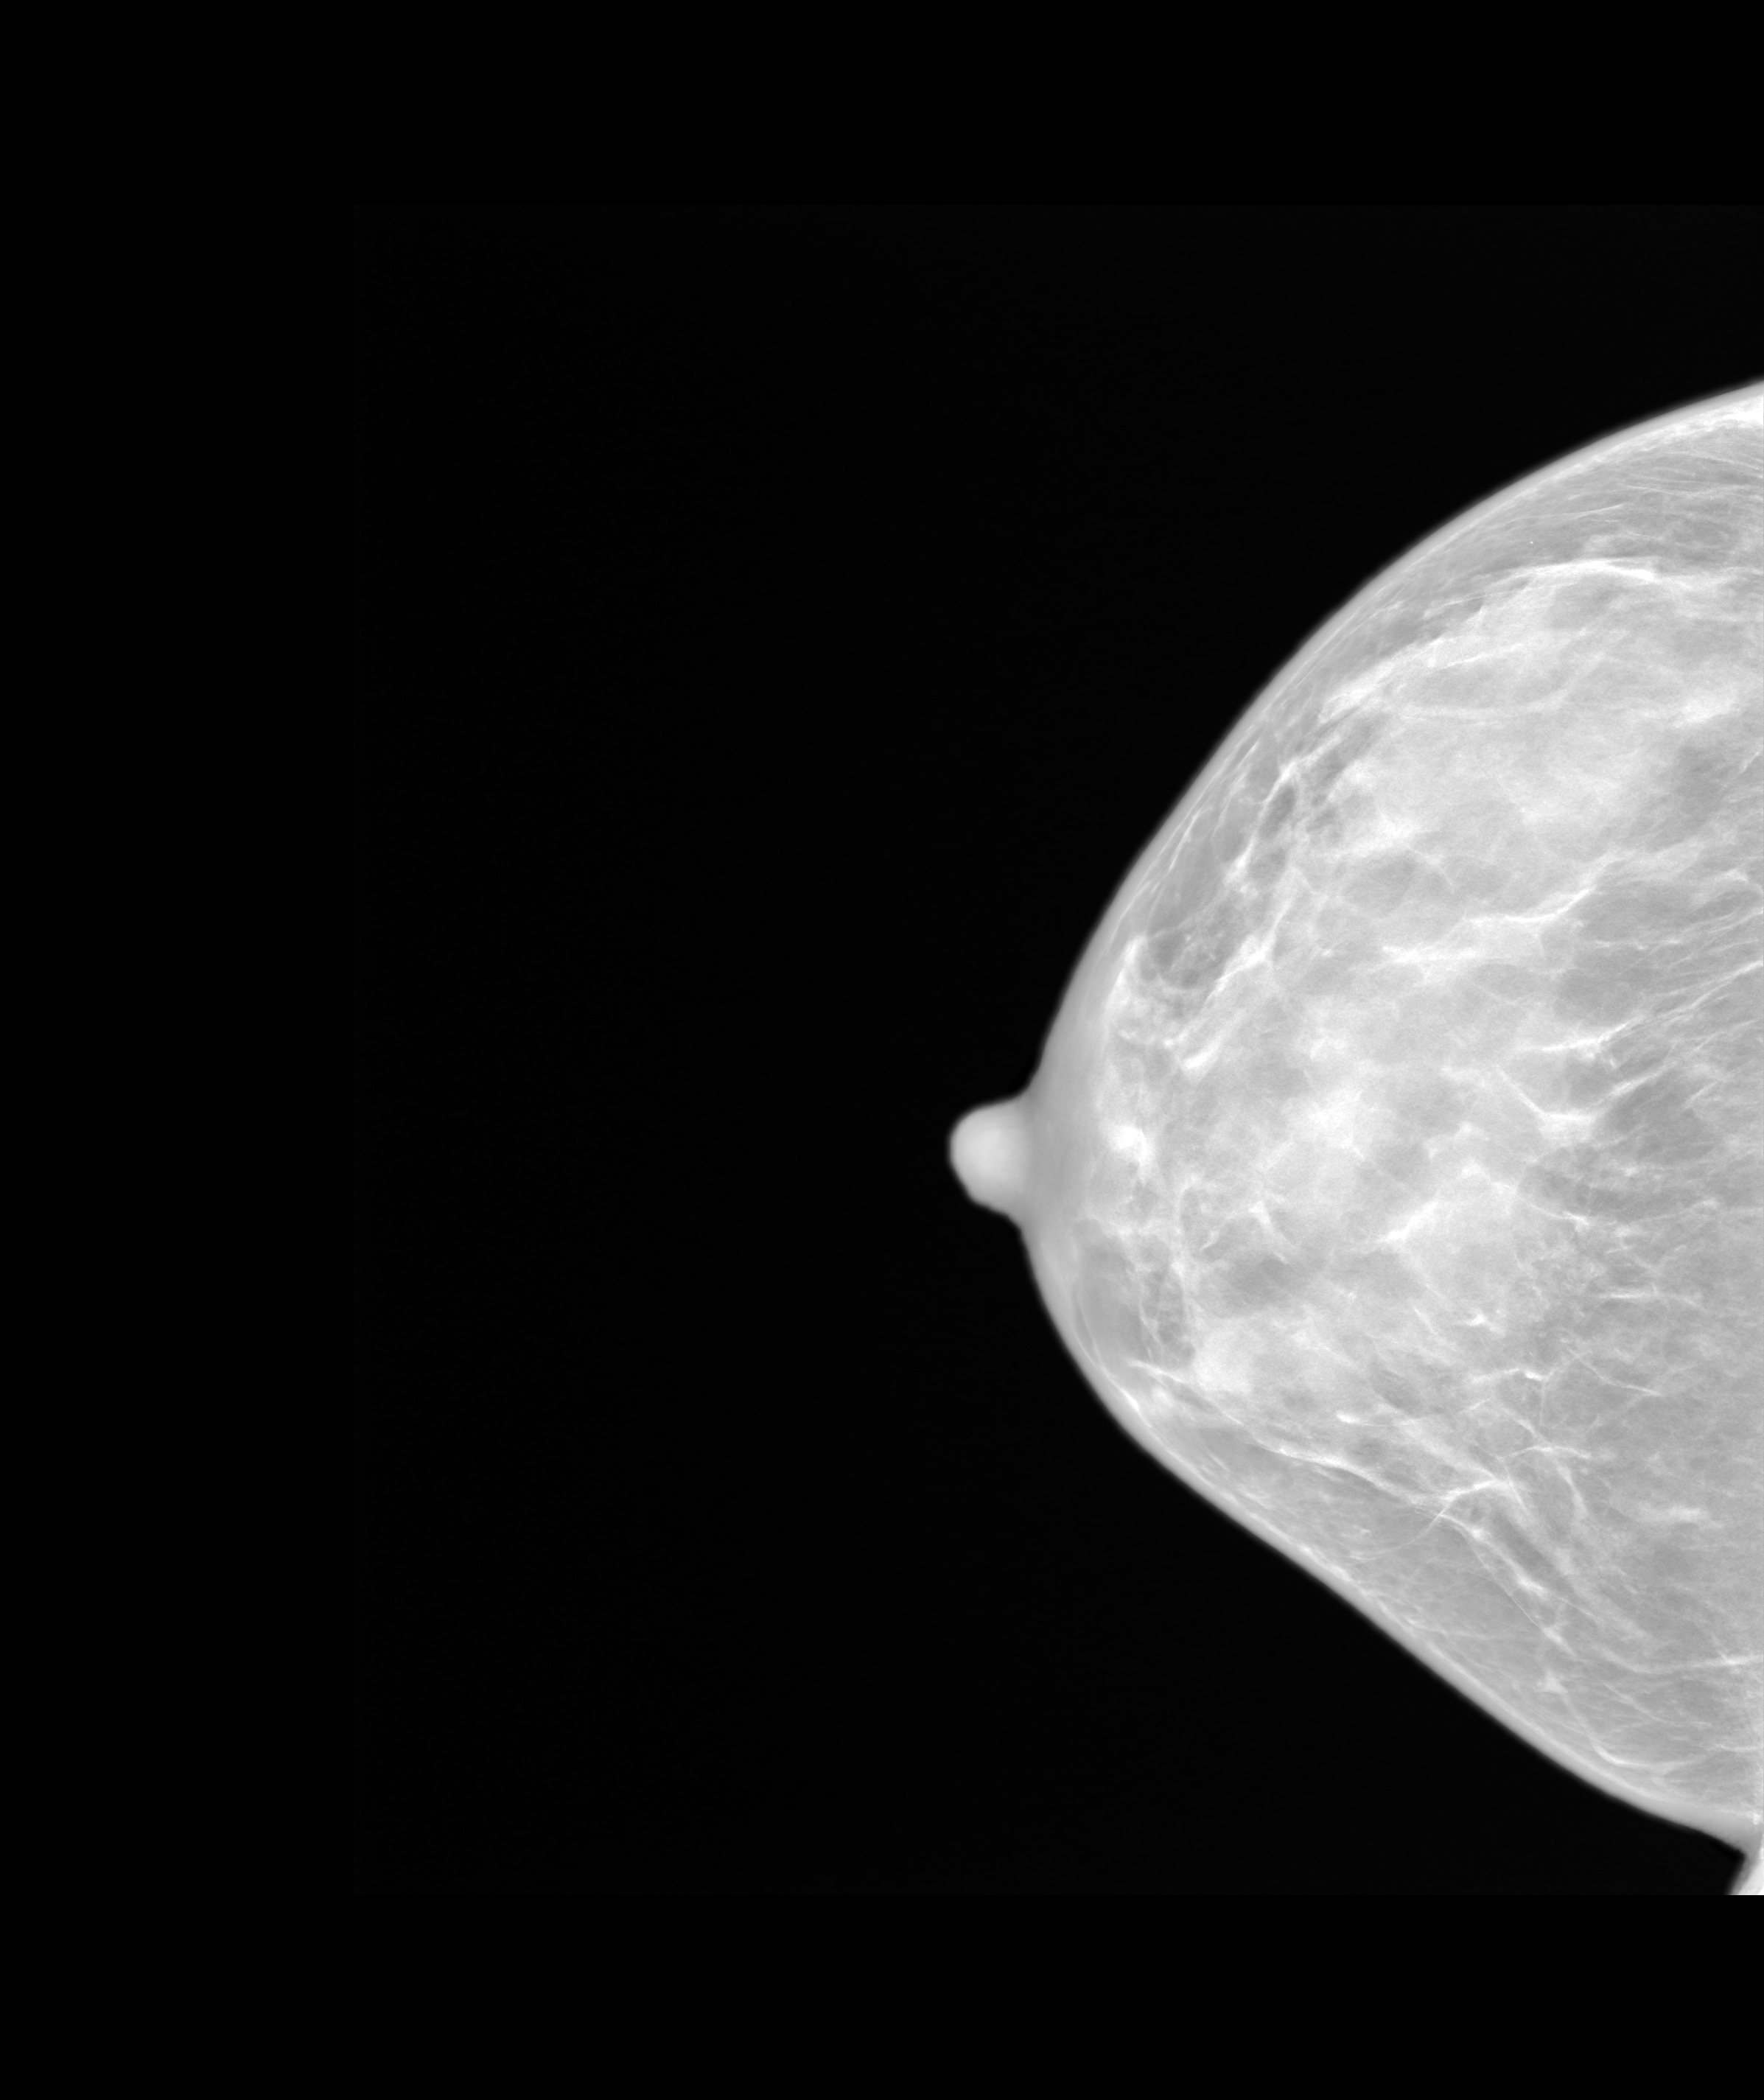
Screening examination. Patient aged 56 years (female).
Image type: synthesized 2-D view from tomosynthesis. Breast: right. Projection: CC view.